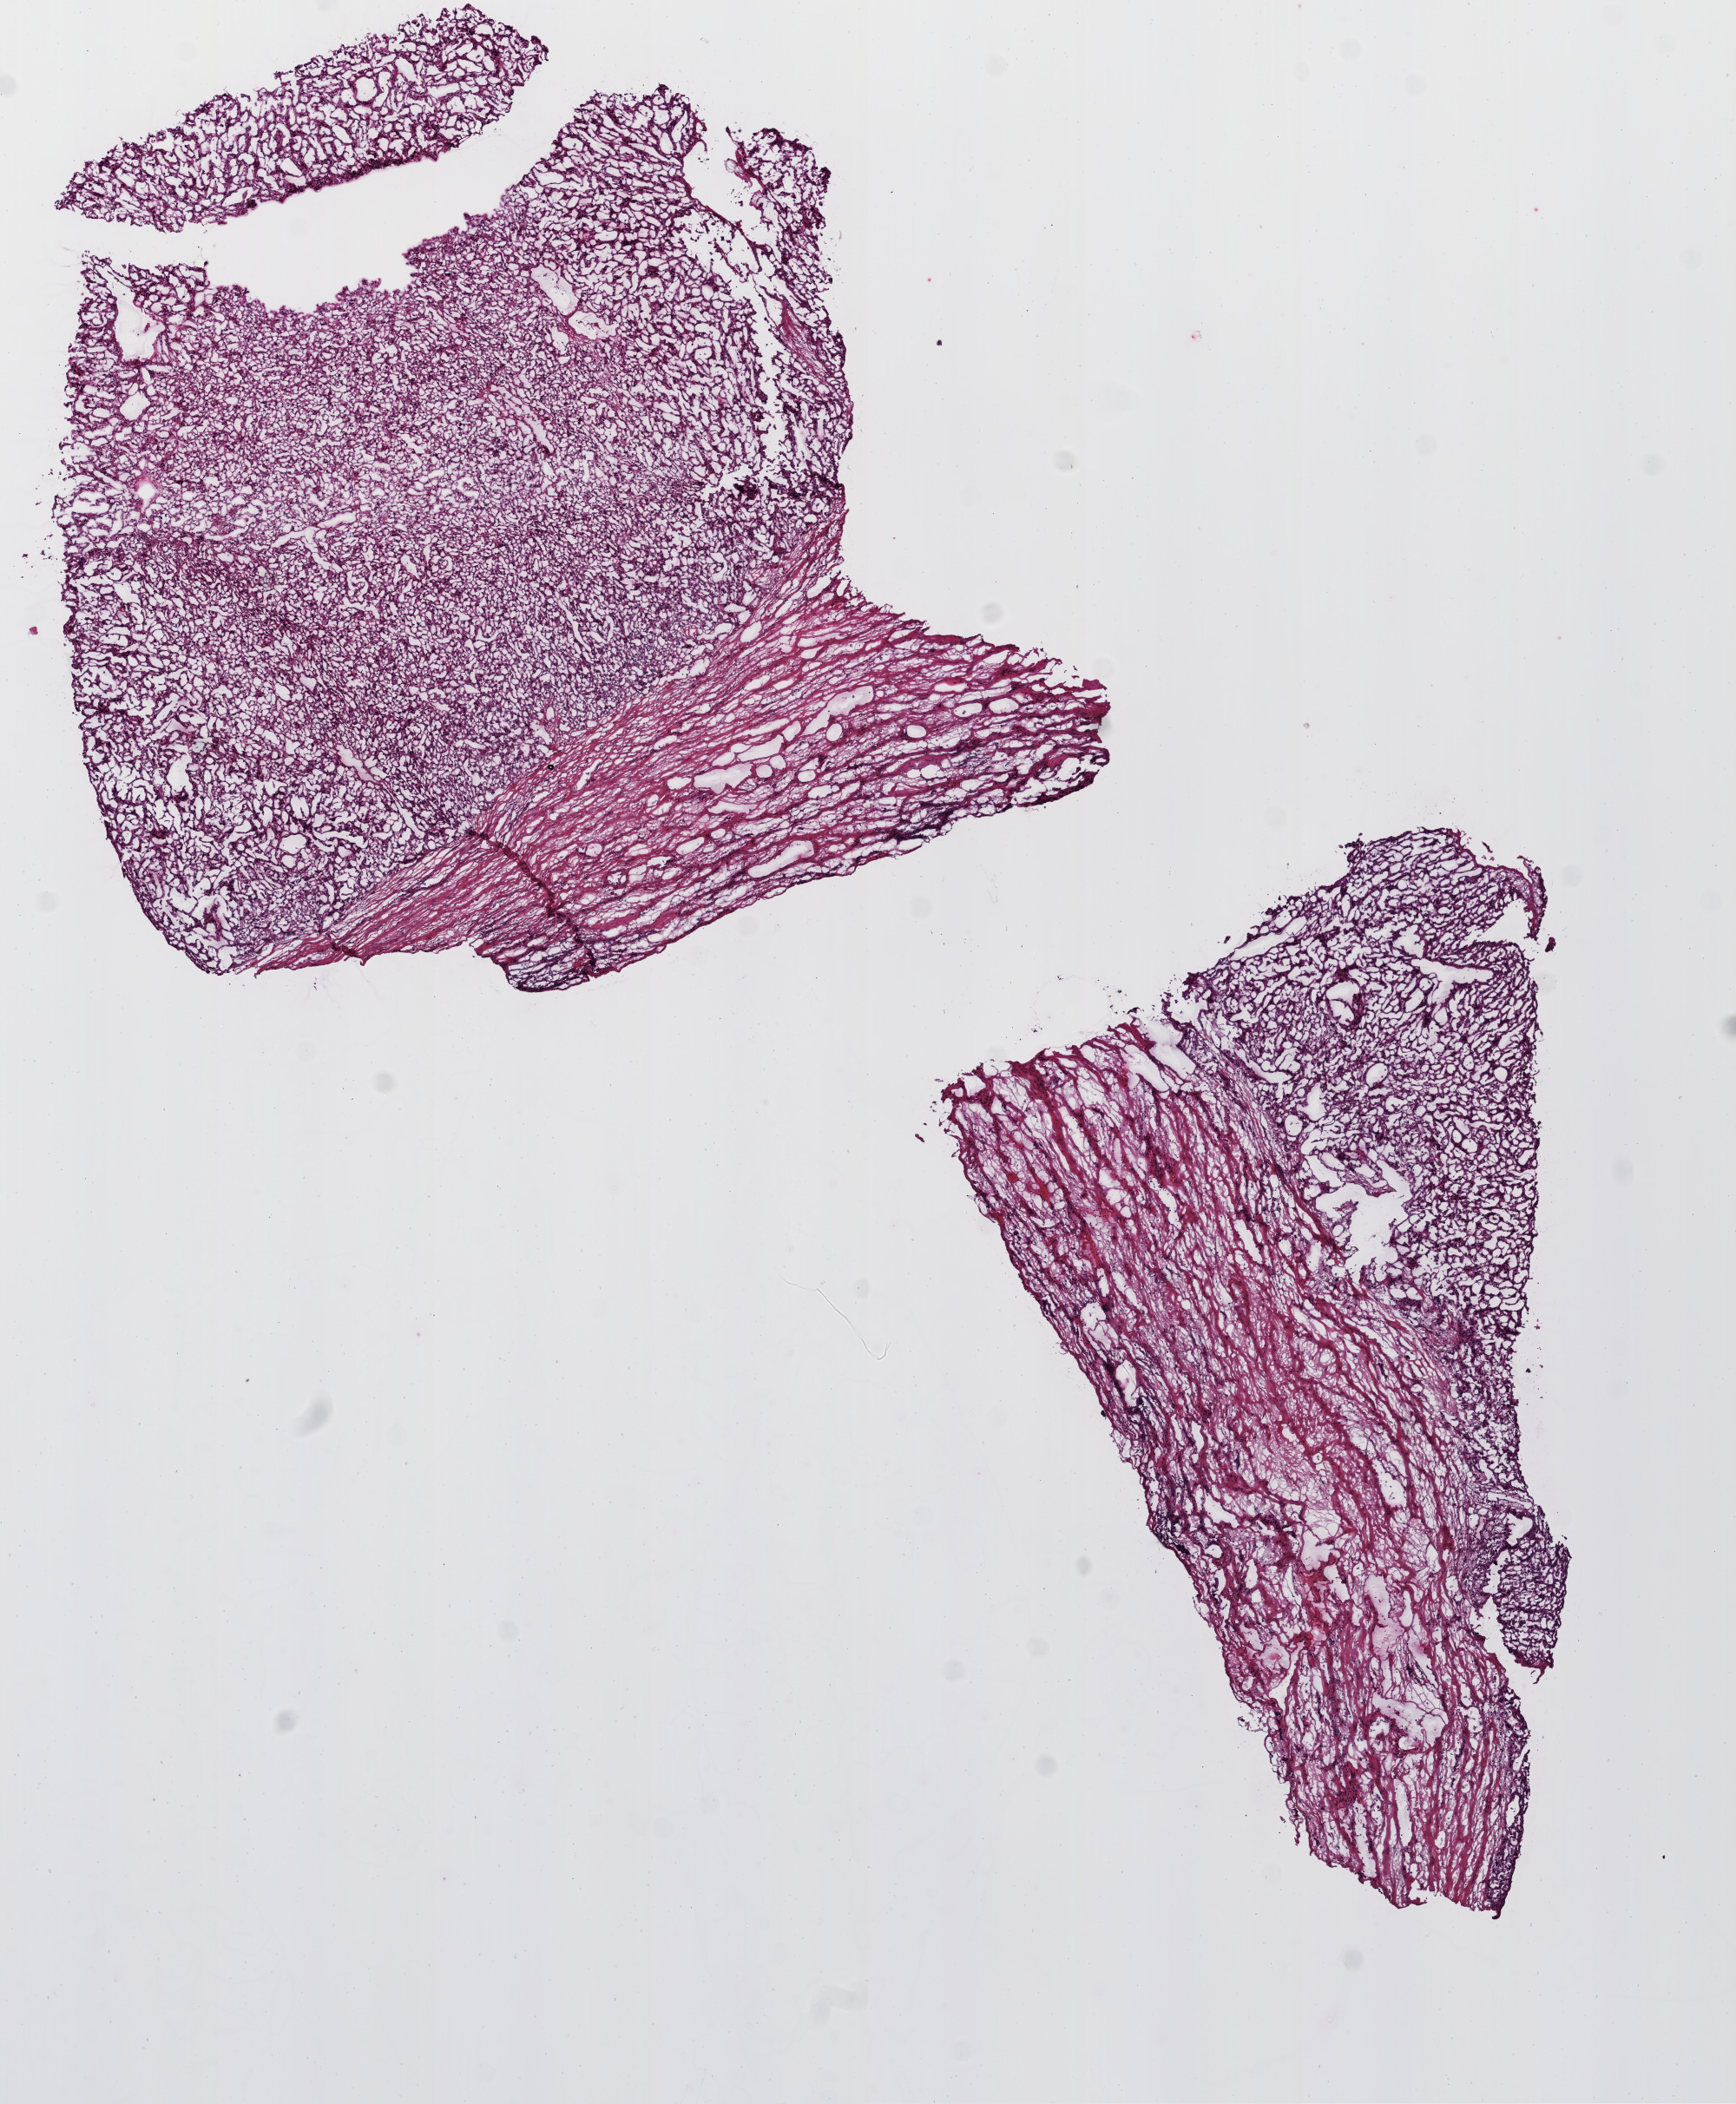
Digitized Hematoxylin and eosin (H&E) stained tissue section (whole slide) — whole scanned area (about 8.0 x 9.7 mm) shown as a low-resolution overview. Frozen section from the top of the tissue portion. Sample: primary tumour, kidney. Patient: male, age at initial diagnosis 48 years. Histologic grade: G3 (poorly differentiated). Slide review estimates, as recorded: tumour cells 60%, tumour nuclei 49%, normal cells 40%, stromal cells 0%, necrosis 0%.
* diagnosis: Clear cell adenocarcinoma, NOS
* AJCC pathologic stage: I